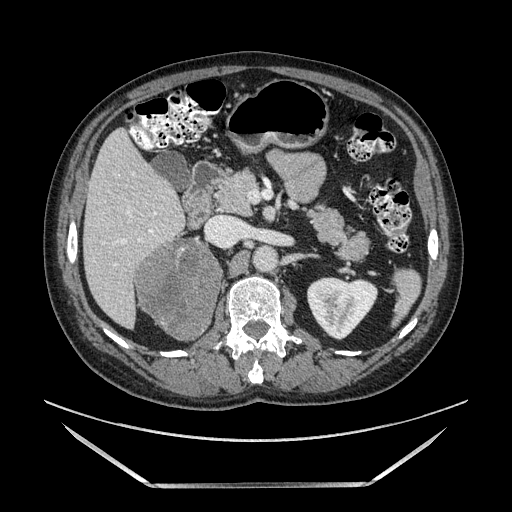
Contrast-enhanced abdominal CT, one axial slice. Slice 70 of 185 in the series (ordered by position). Soft-tissue window (W 400 / L 40 HU). 1.25 mm slice thickness. 512 × 512 image matrix, field of view 440 × 440 mm. Male patient. From the clinical record (not read from this slice): diagnosis: adrenocortical carcinoma; tumour side: right adrenal; tumour size at pathology: 10.3 cm; Ki-67 index: 20 %; stage (as recorded): 3.
Outlined on this slice (semi-automatic segmentation, software-assisted and operator-edited):
- mass: bounding box <135,240,221,337> (left, top, right, bottom; pixels)